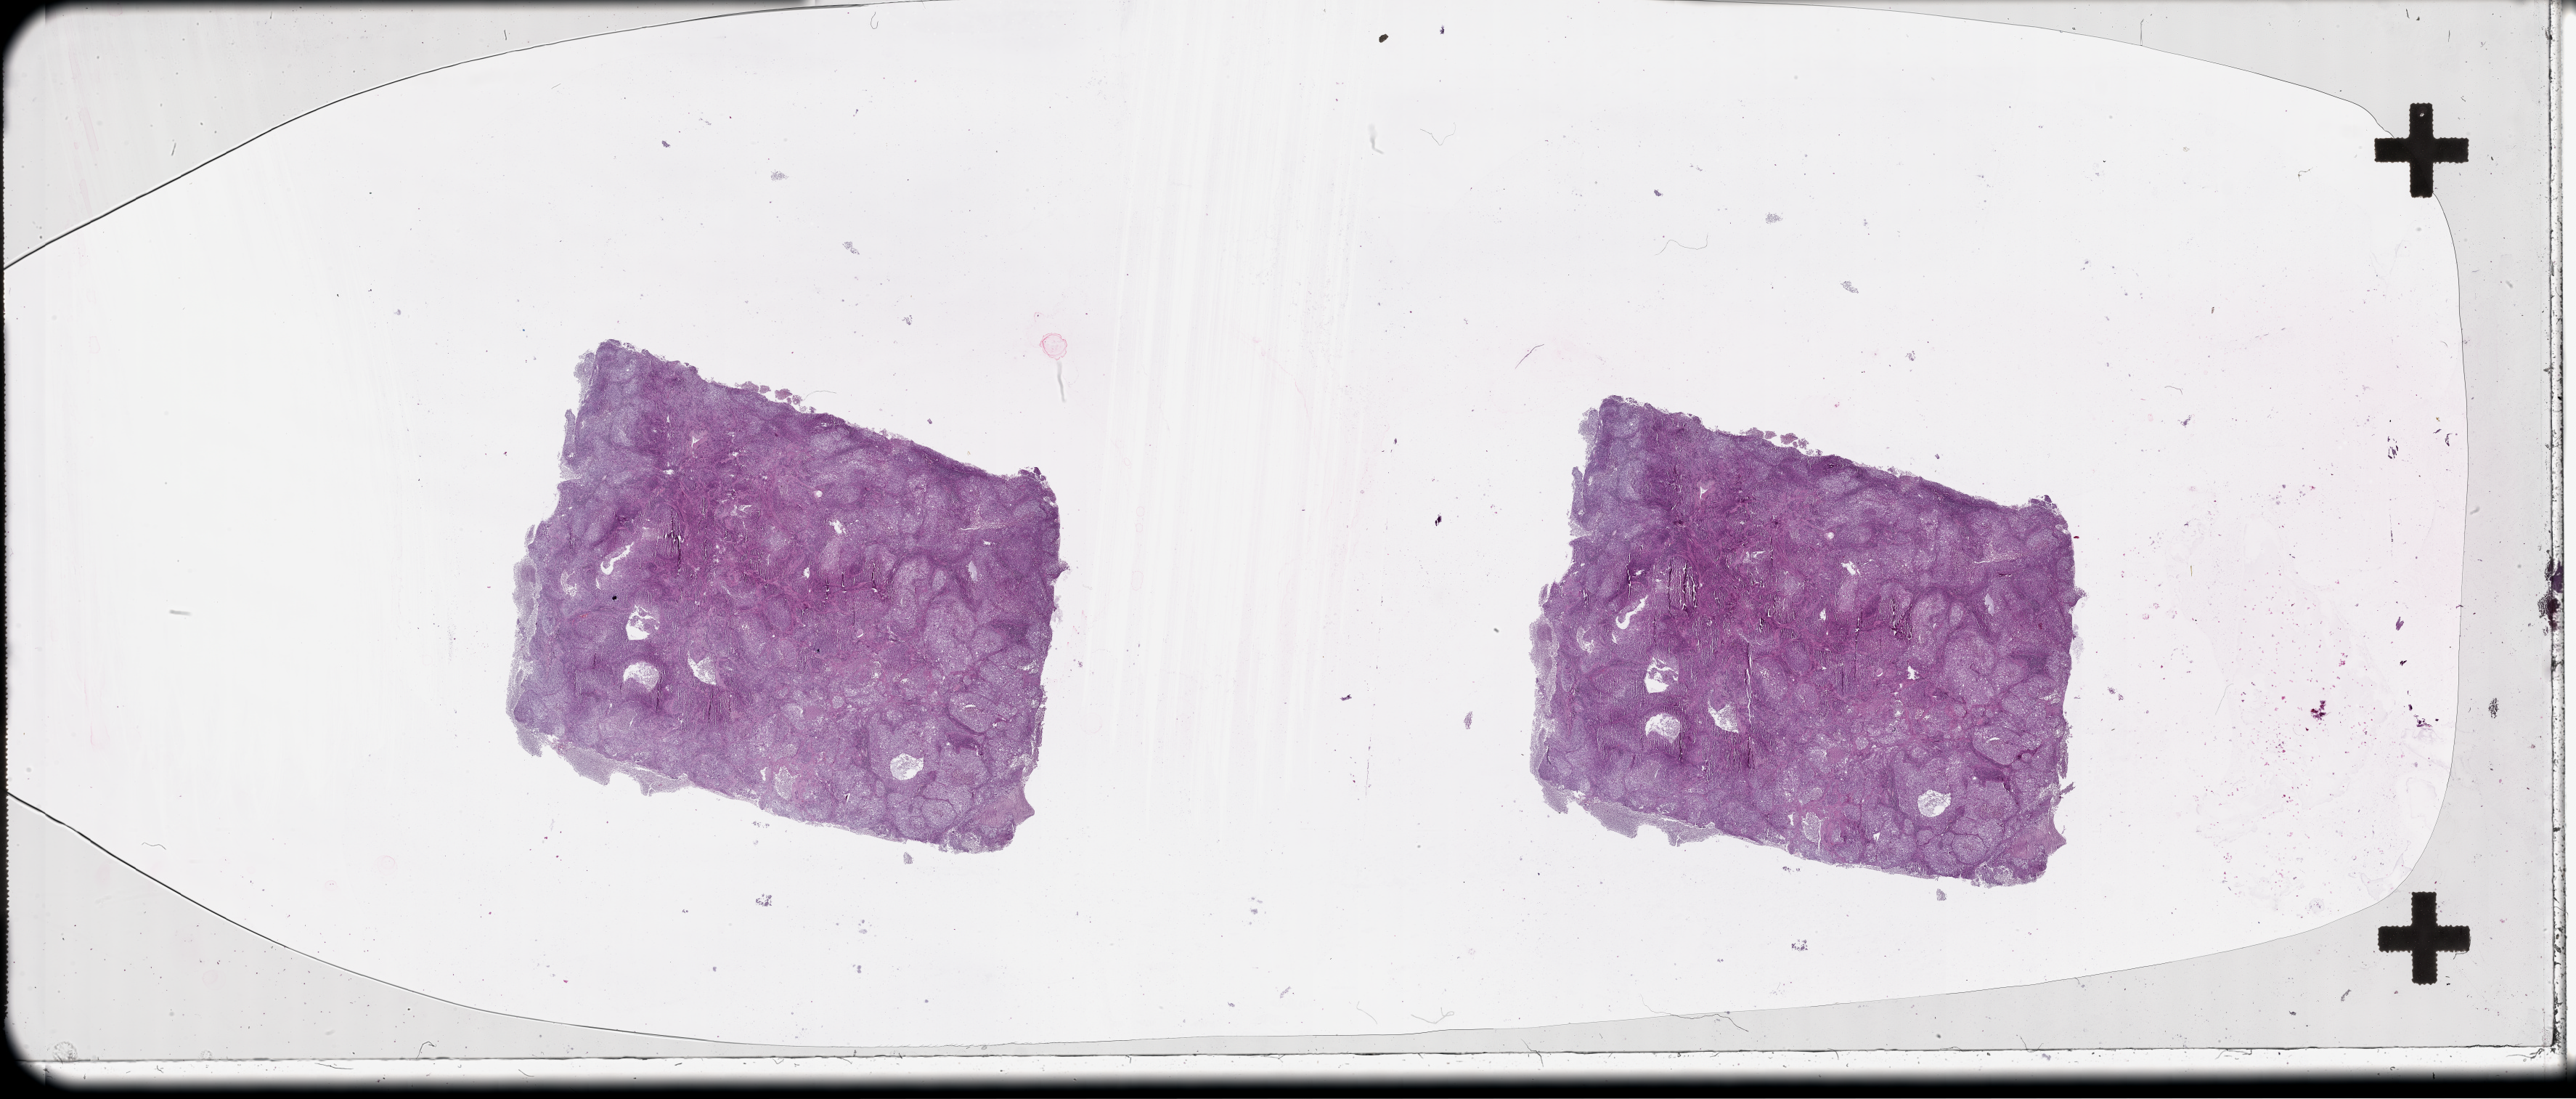
Hematoxylin and eosin (H&E) stained whole-slide image, shown as a low-resolution overview of the whole scanned area (about 57.1 x 24.4 mm, slide scanned at 20x); tumour tissue sample, lung. Patient: female, age 72 years.
* patient diagnosis (cohort enrolment): squamous cell carcinoma (lung)